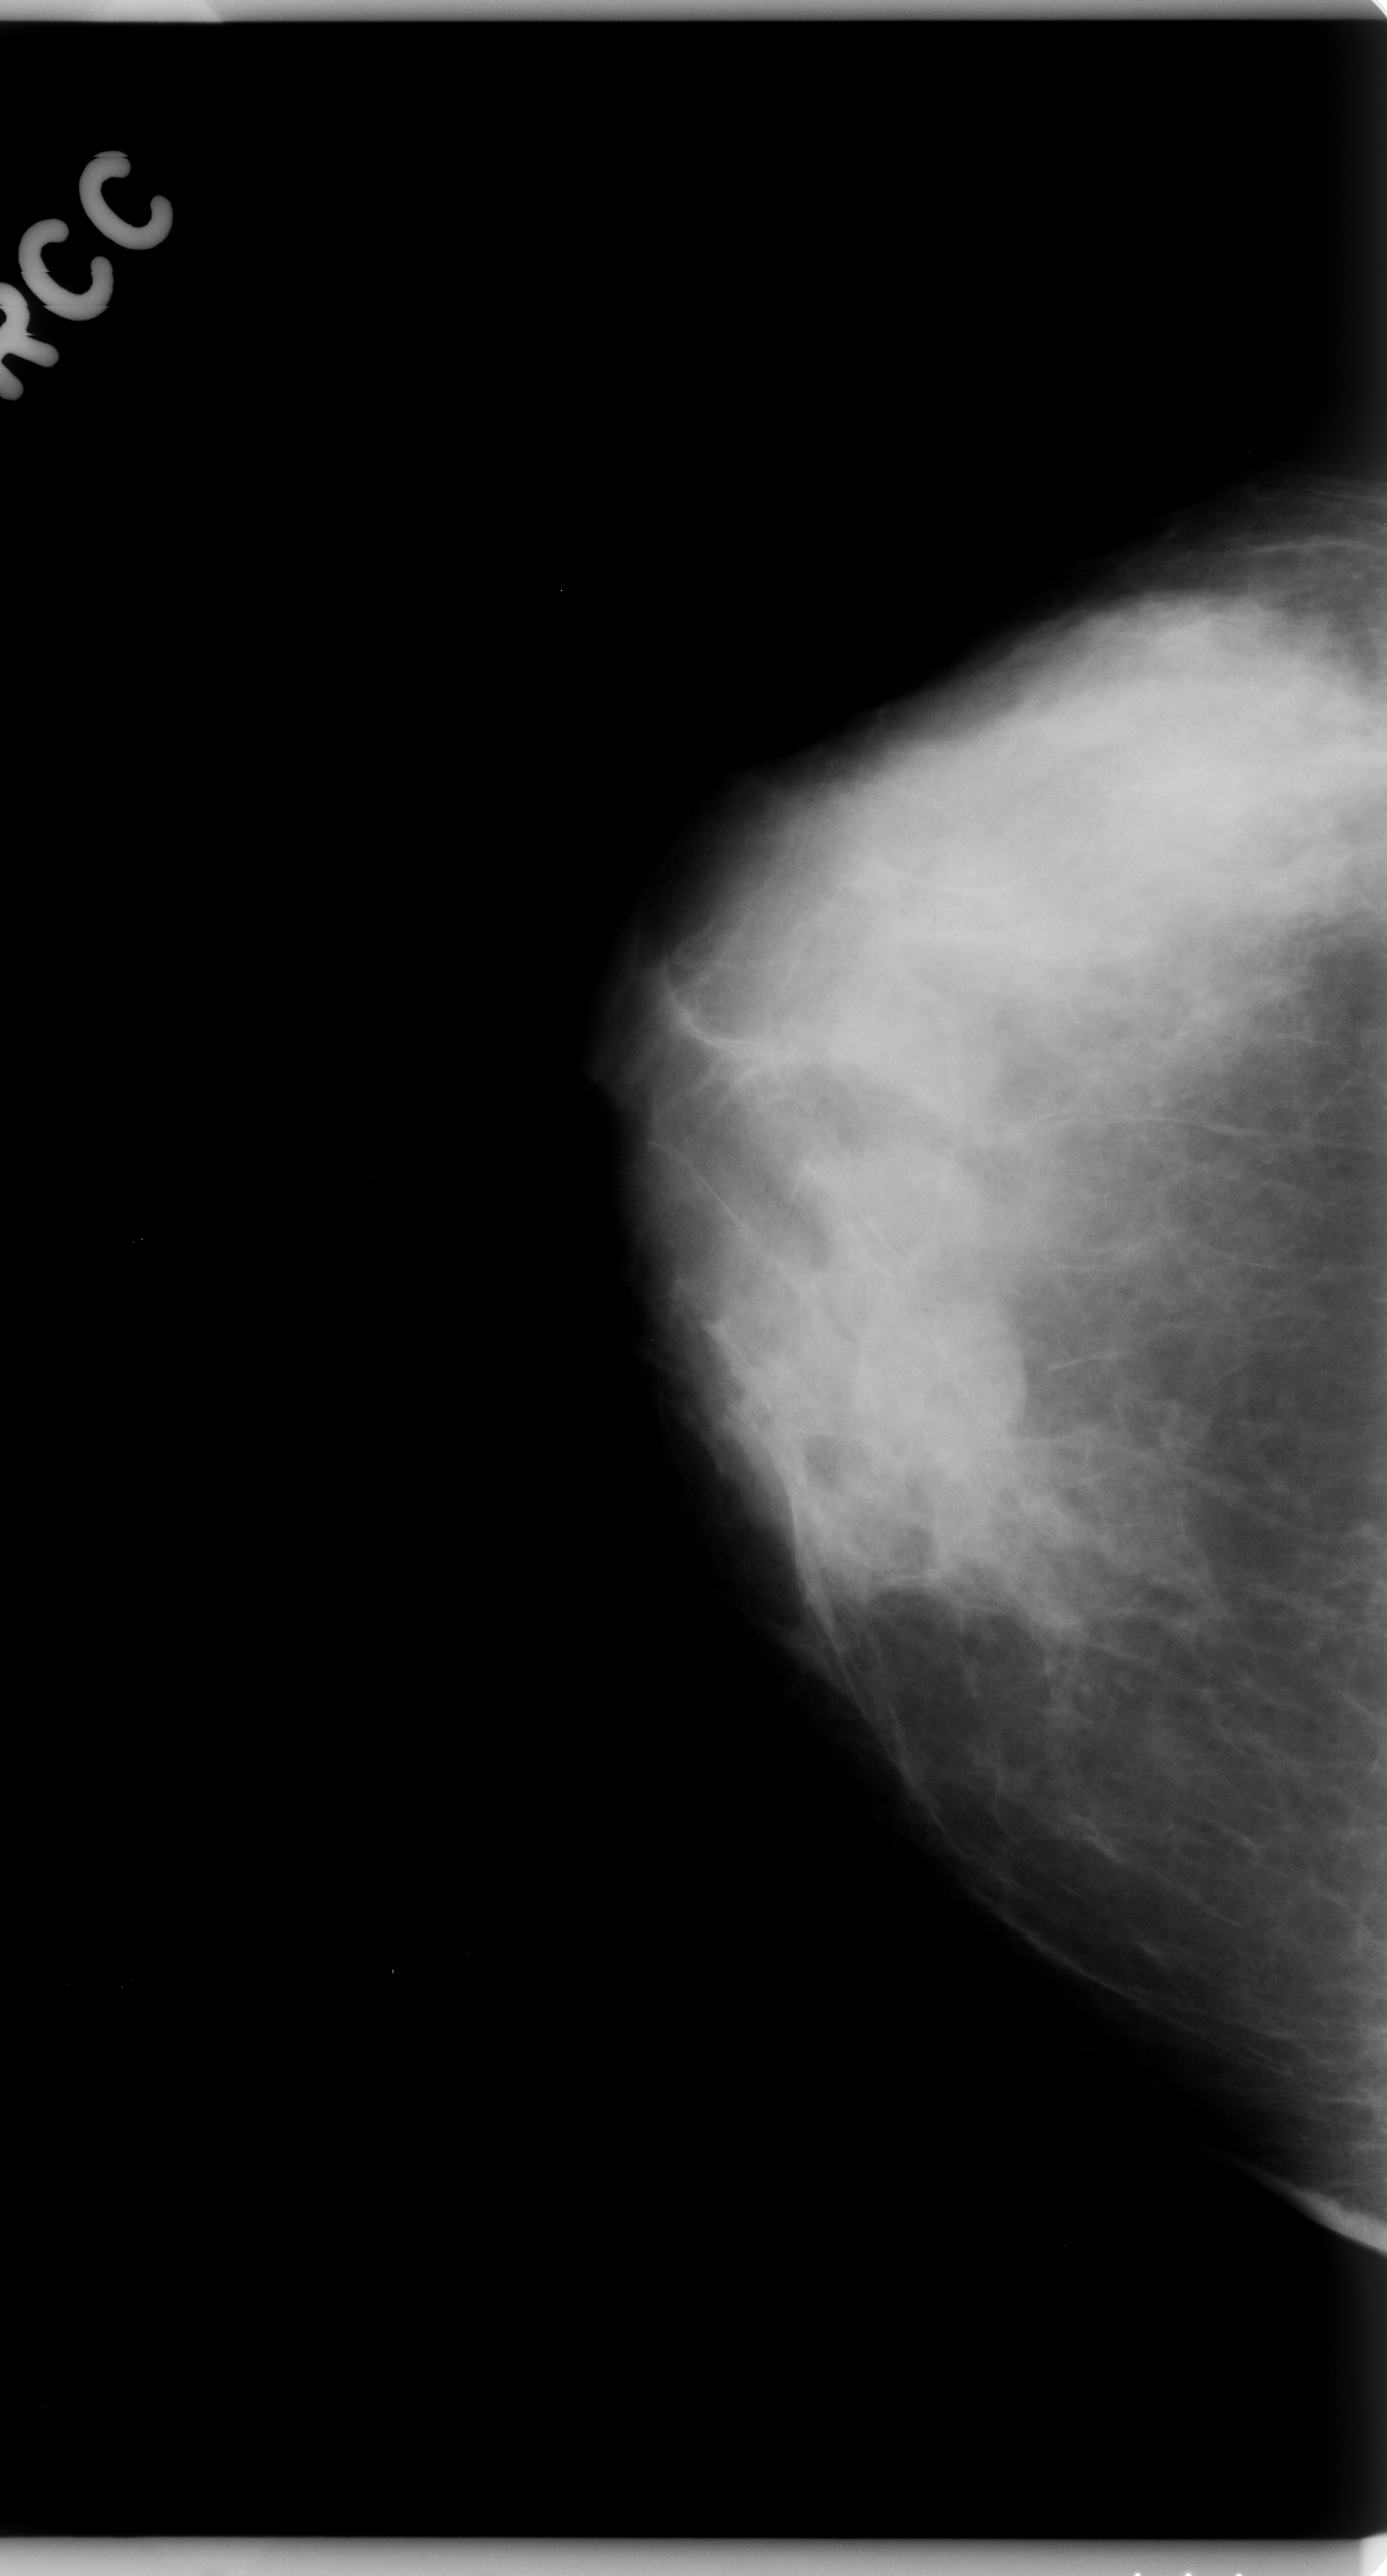
Scanned film-screen mammogram; right breast; CC view; breast composition: heterogeneously dense (BI-RADS density category 3 of 4).
- Abnormality record for this image: mass, shape round, margins obscured; BI-RADS assessment category 3; subtlety rating 4 on a 1 (subtle) to 5 (obvious) scale; pathology result (as recorded, not read from the image): benign.